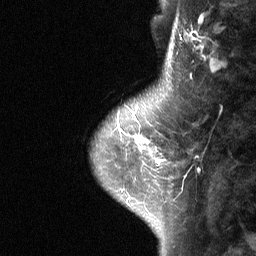
Breast MRI (dynamic contrast-enhanced), one sagittal slice. Slice 15 of 64 in the series (ordered by position). Dynamic contrast-enhanced study with each time point stored as its own series, time point 2 of 3 at this slice position (early post-contrast, ordered by acquisition time). 1.5 T. TE 4.8 ms, TR 27 ms. 2 mm slice thickness. 256 × 256 image matrix. Patient: female, 42 years. From the clinical record (not read from this slice): setting: breast cancer imaged before/during neoadjuvant chemotherapy; receptor status: triple-negative.
Structures marked on this image (semi-automatic segmentation, software-assisted and operator-edited):
- analysis volume of interest (the breast-tissue region the enhancement analysis was run in; not a lesion): box from (x=111, y=104) to (x=177, y=178) px
- tumour enhancement mask (voxels above the 90 % enhancement threshold inside the analysis volume of interest): (x=124, y=133)–(x=163, y=164)